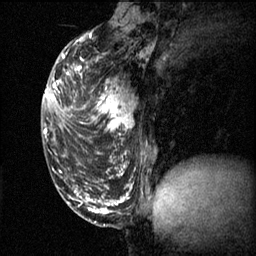
Breast MRI (dynamic contrast-enhanced), one sagittal slice; 3 images stored at this slice position (order not interpretable as contrast timing); 1.5 T; TE 4.2 ms, TR 11.1 ms; 2 mm slice thickness; 256 × 256 image matrix, field of view 180 × 180 mm. Female patient, age 50 years.
Annotated regions visible in this slice (semi-automatically segmented with operator editing):
- analysis volume of interest (the breast-tissue region the enhancement analysis was run in; not a lesion): bounding box <68,68,141,141> (left, top, right, bottom; pixels)
- tumour enhancement mask (voxels above the 70 % enhancement threshold inside the analysis volume of interest): <68,68,133,133>